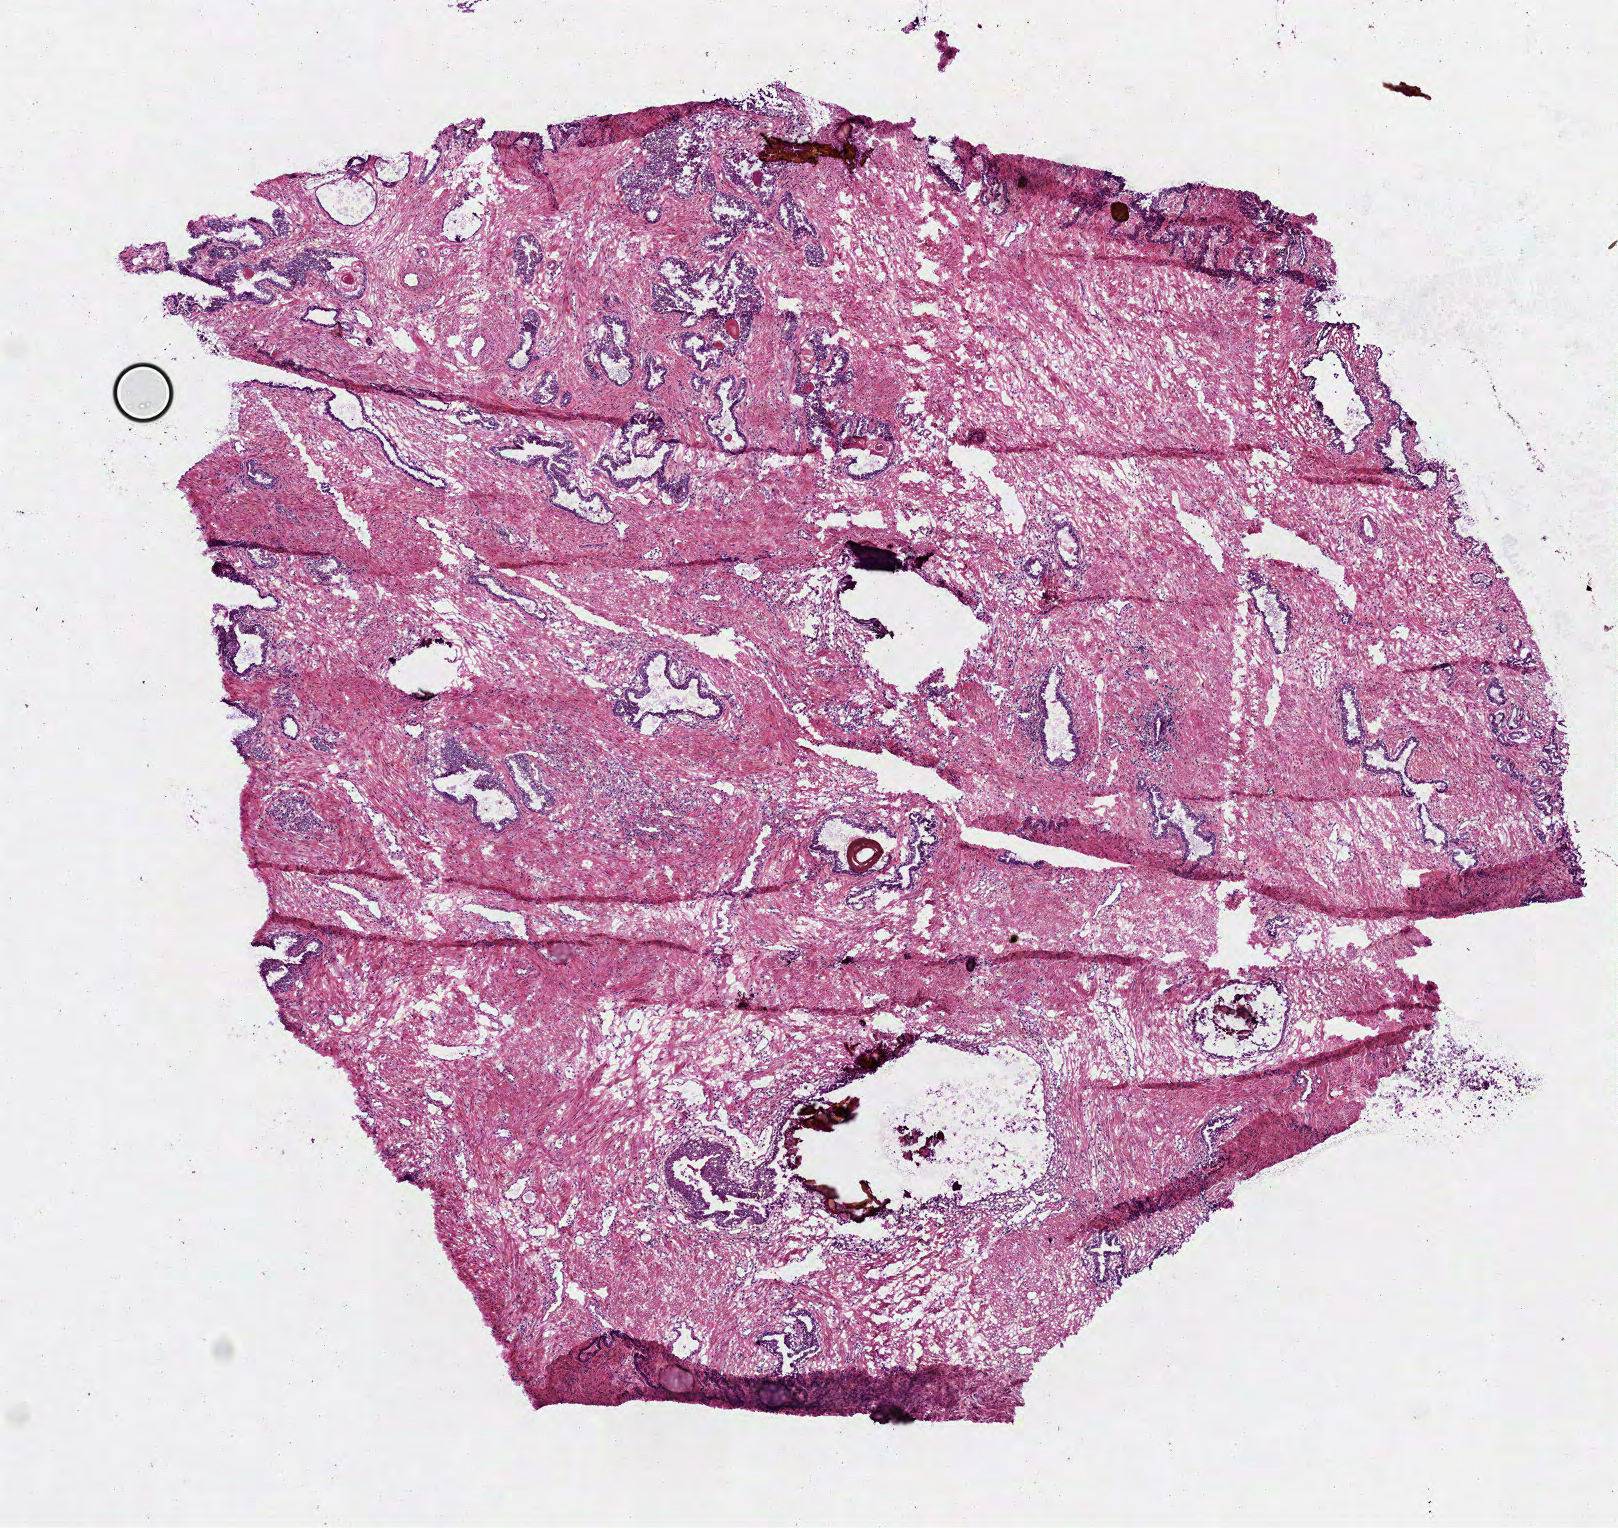
Digitized Hematoxylin and eosin (H&E) stained tissue section (whole slide) — shown as a low-resolution overview of the whole scanned area (about 6.5 x 6.2 mm, slide scanned at 40x), frozen section, primary tumour sample from the prostate. Male, age 52 years at initial diagnosis. Gleason score: 7 (3+4). Slide review estimates, as recorded: tumour cells 3%, tumour nuclei 3%, normal cells 25%, stromal cells 72%, necrosis 0%. Inflammatory infiltration, as recorded: lymphocyte infiltration 3%, monocyte infiltration 3%, neutrophil infiltration 0%.
Pathologic diagnosis: Acinar cell carcinoma (prostate gland).